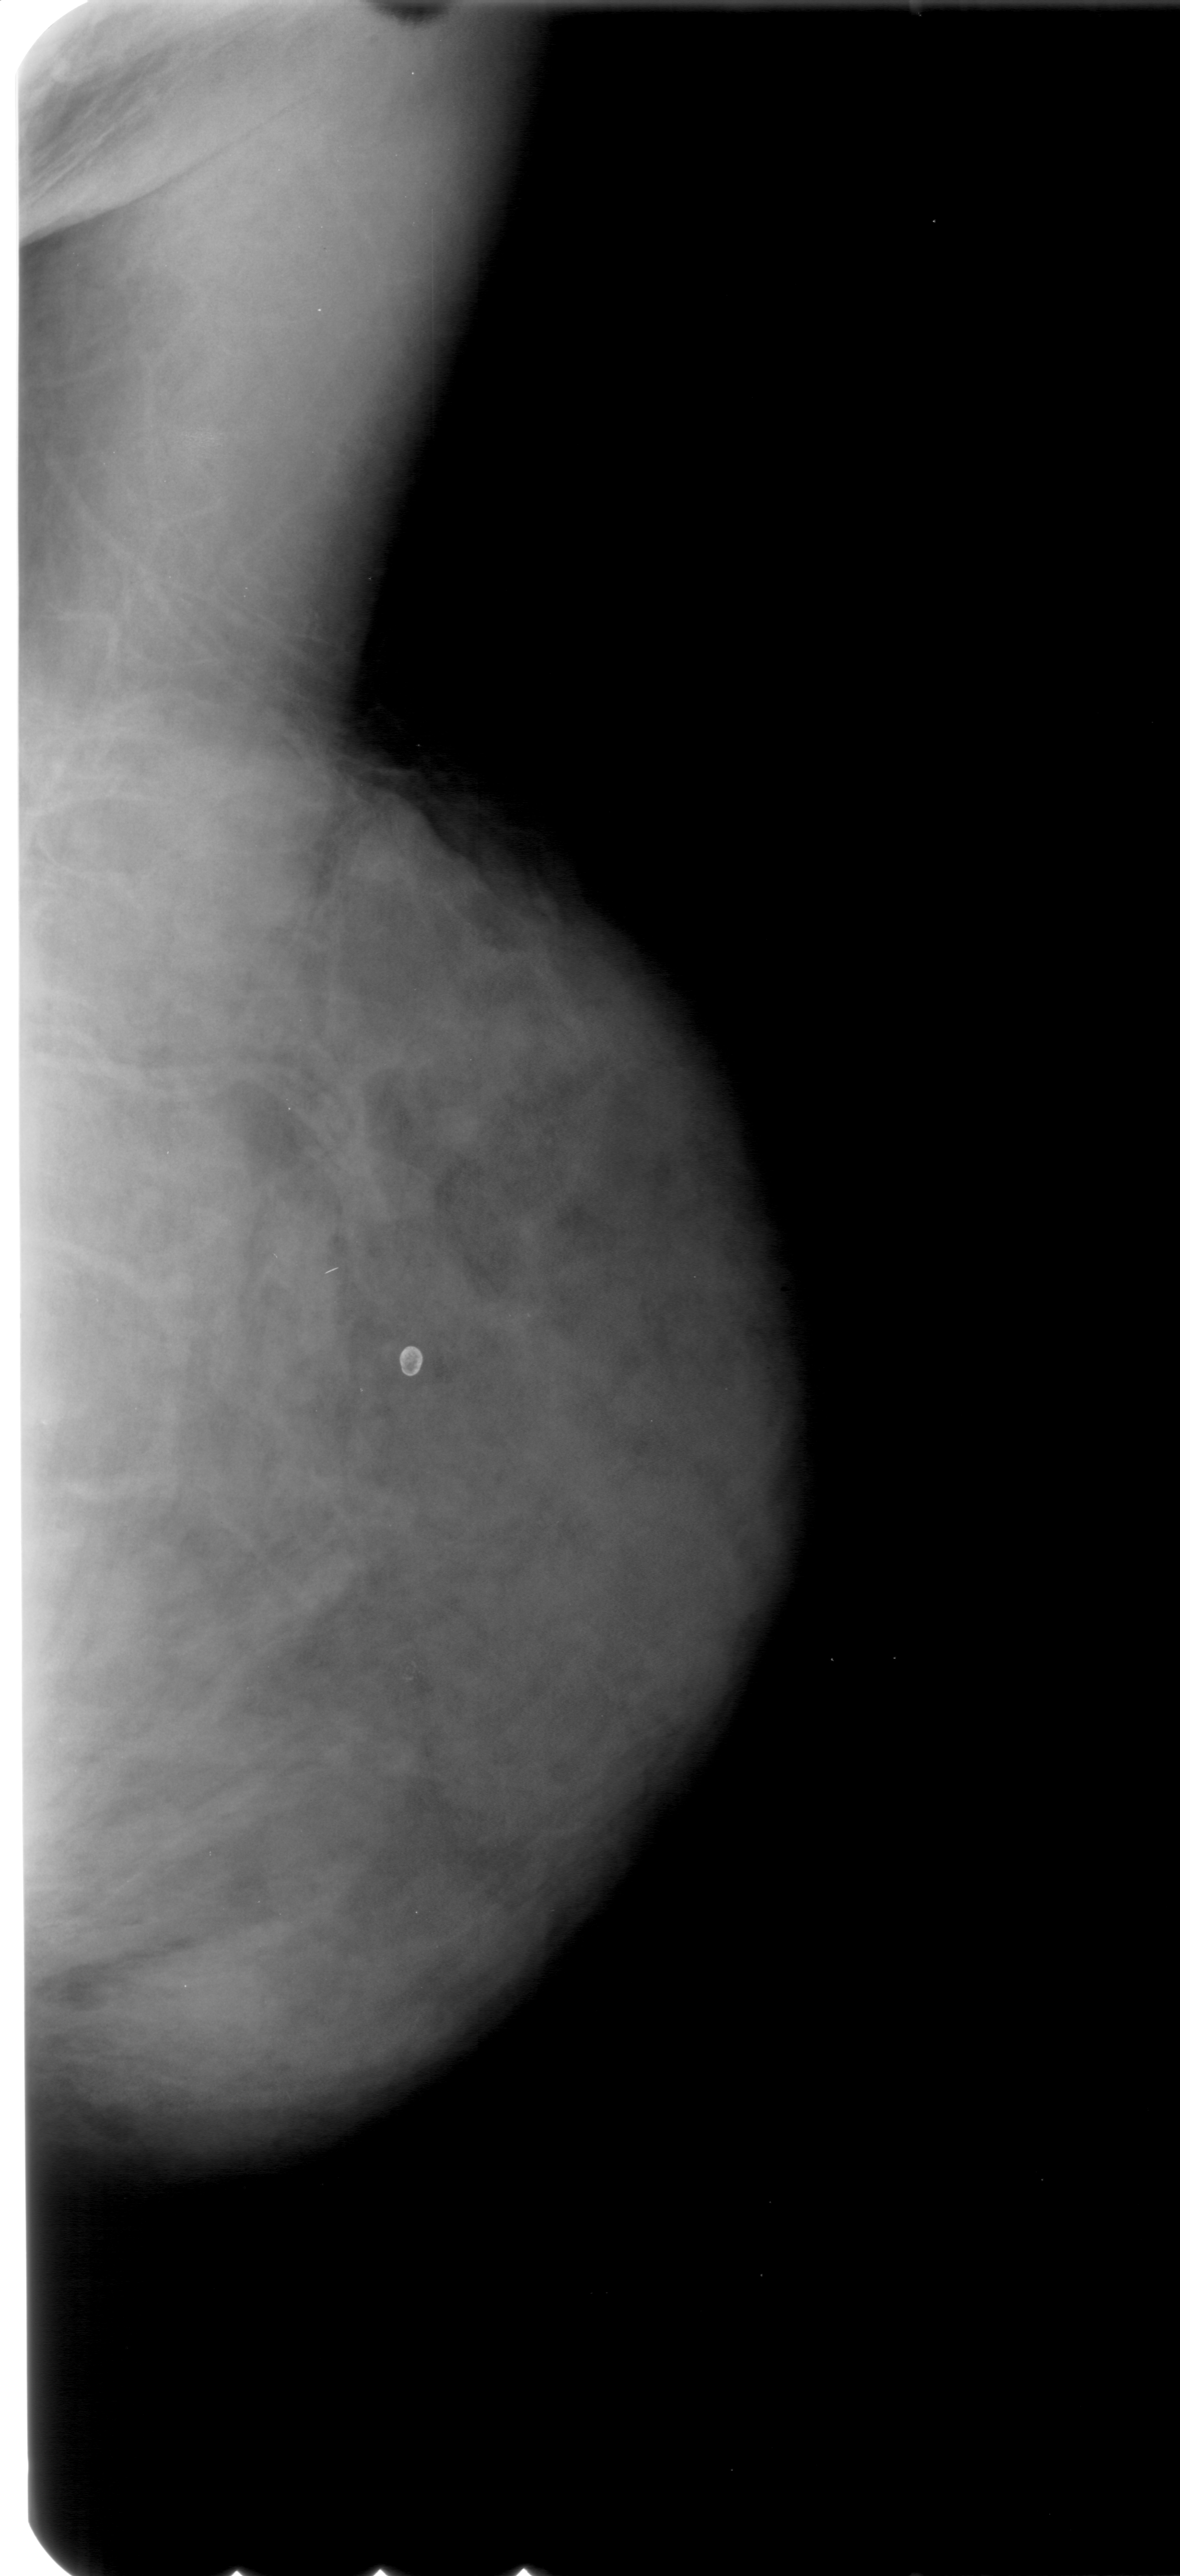
Mammogram (digitized film). Right breast. Mediolateral oblique (MLO) view. 1180 × 2576 image matrix.
Expert-marked regions of interest on this image (one box per marked abnormality):
- calcifications, morphology pleomorphic, distribution clustered; BI-RADS assessment category 3; subtlety rating 1 on a 1 (subtle) to 5 (obvious) scale; pathology (as recorded): benign: box from (x=397, y=1651) to (x=448, y=1703) px